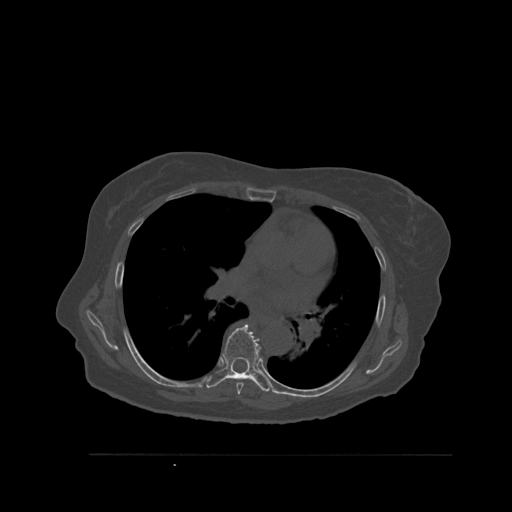
CT including the spine, one axial slice; slice 370 of 527 in the series (ordered by position); bone window (W 1800 / L 400 HU); 1.5 mm slice thickness; 512 × 512 image matrix. Female patient, age 73 years. Case-level facts recorded for this patient, not image findings: primary cancer: breast.
Structures marked on this image (semi-automatic segmentation, software-assisted and operator-edited):
- T6 vertebra: bounding box [x1, y1, x2, y2] px = [236, 383, 244, 395]
- T7 vertebra: [204, 324, 271, 392]